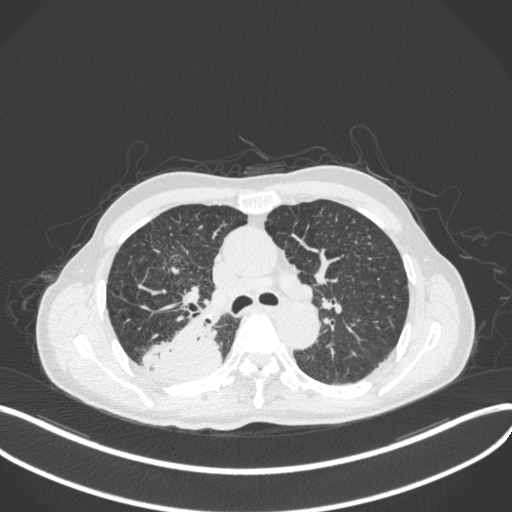
Chest CT, one axial slice; slice 298 of 423 in the series (ordered by position); 120 kVp; lung window (W 1500 / L -600 HU); 512 × 512 image matrix, field of view 400 × 400 mm. Male patient, age 79 years. Case-level facts recorded for this patient, not image findings: clinical TNM (as recorded): T3 N0 M0.
Annotated regions visible in this slice (bounding box drawn by a radiologist):
- lung tumour (recorded histology: adenocarcinoma): box from (x=139, y=317) to (x=225, y=383) px